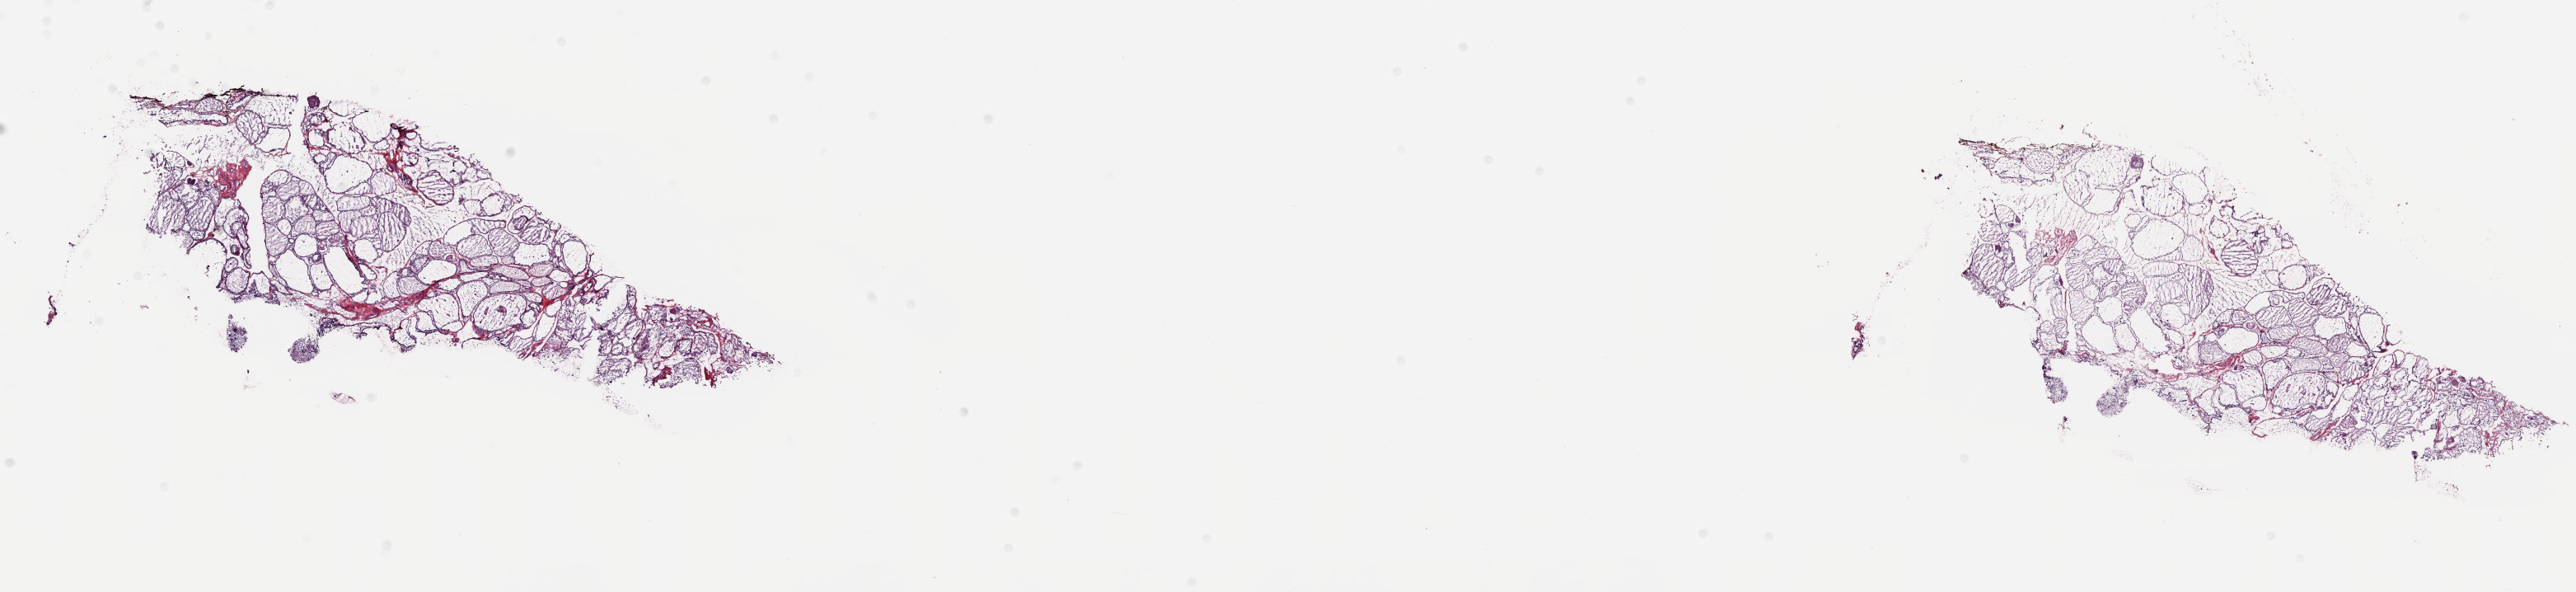
Whole-slide histology image, Hematoxylin and eosin (H&E) stained, whole scanned area (about 24.8 x 5.7 mm) shown as a low-resolution overview, frozen section from the top of the tissue portion, sample: solid tissue normal (non-tumour tissue), thyroid. Female, age 39 years at initial diagnosis. Pathologist review of this section (percent, as recorded): tumour cells 0%, tumour nuclei 0%, normal cells 100%, stromal cells 0%, necrosis 0%. Inflammatory infiltration, as recorded: lymphocyte infiltration 2%, monocyte infiltration 2%, neutrophil infiltration 0%.
This section: solid tissue normal (non-tumour) sample from the same patient. Patient diagnosis: Papillary carcinoma, columnar cell (thyroid gland).